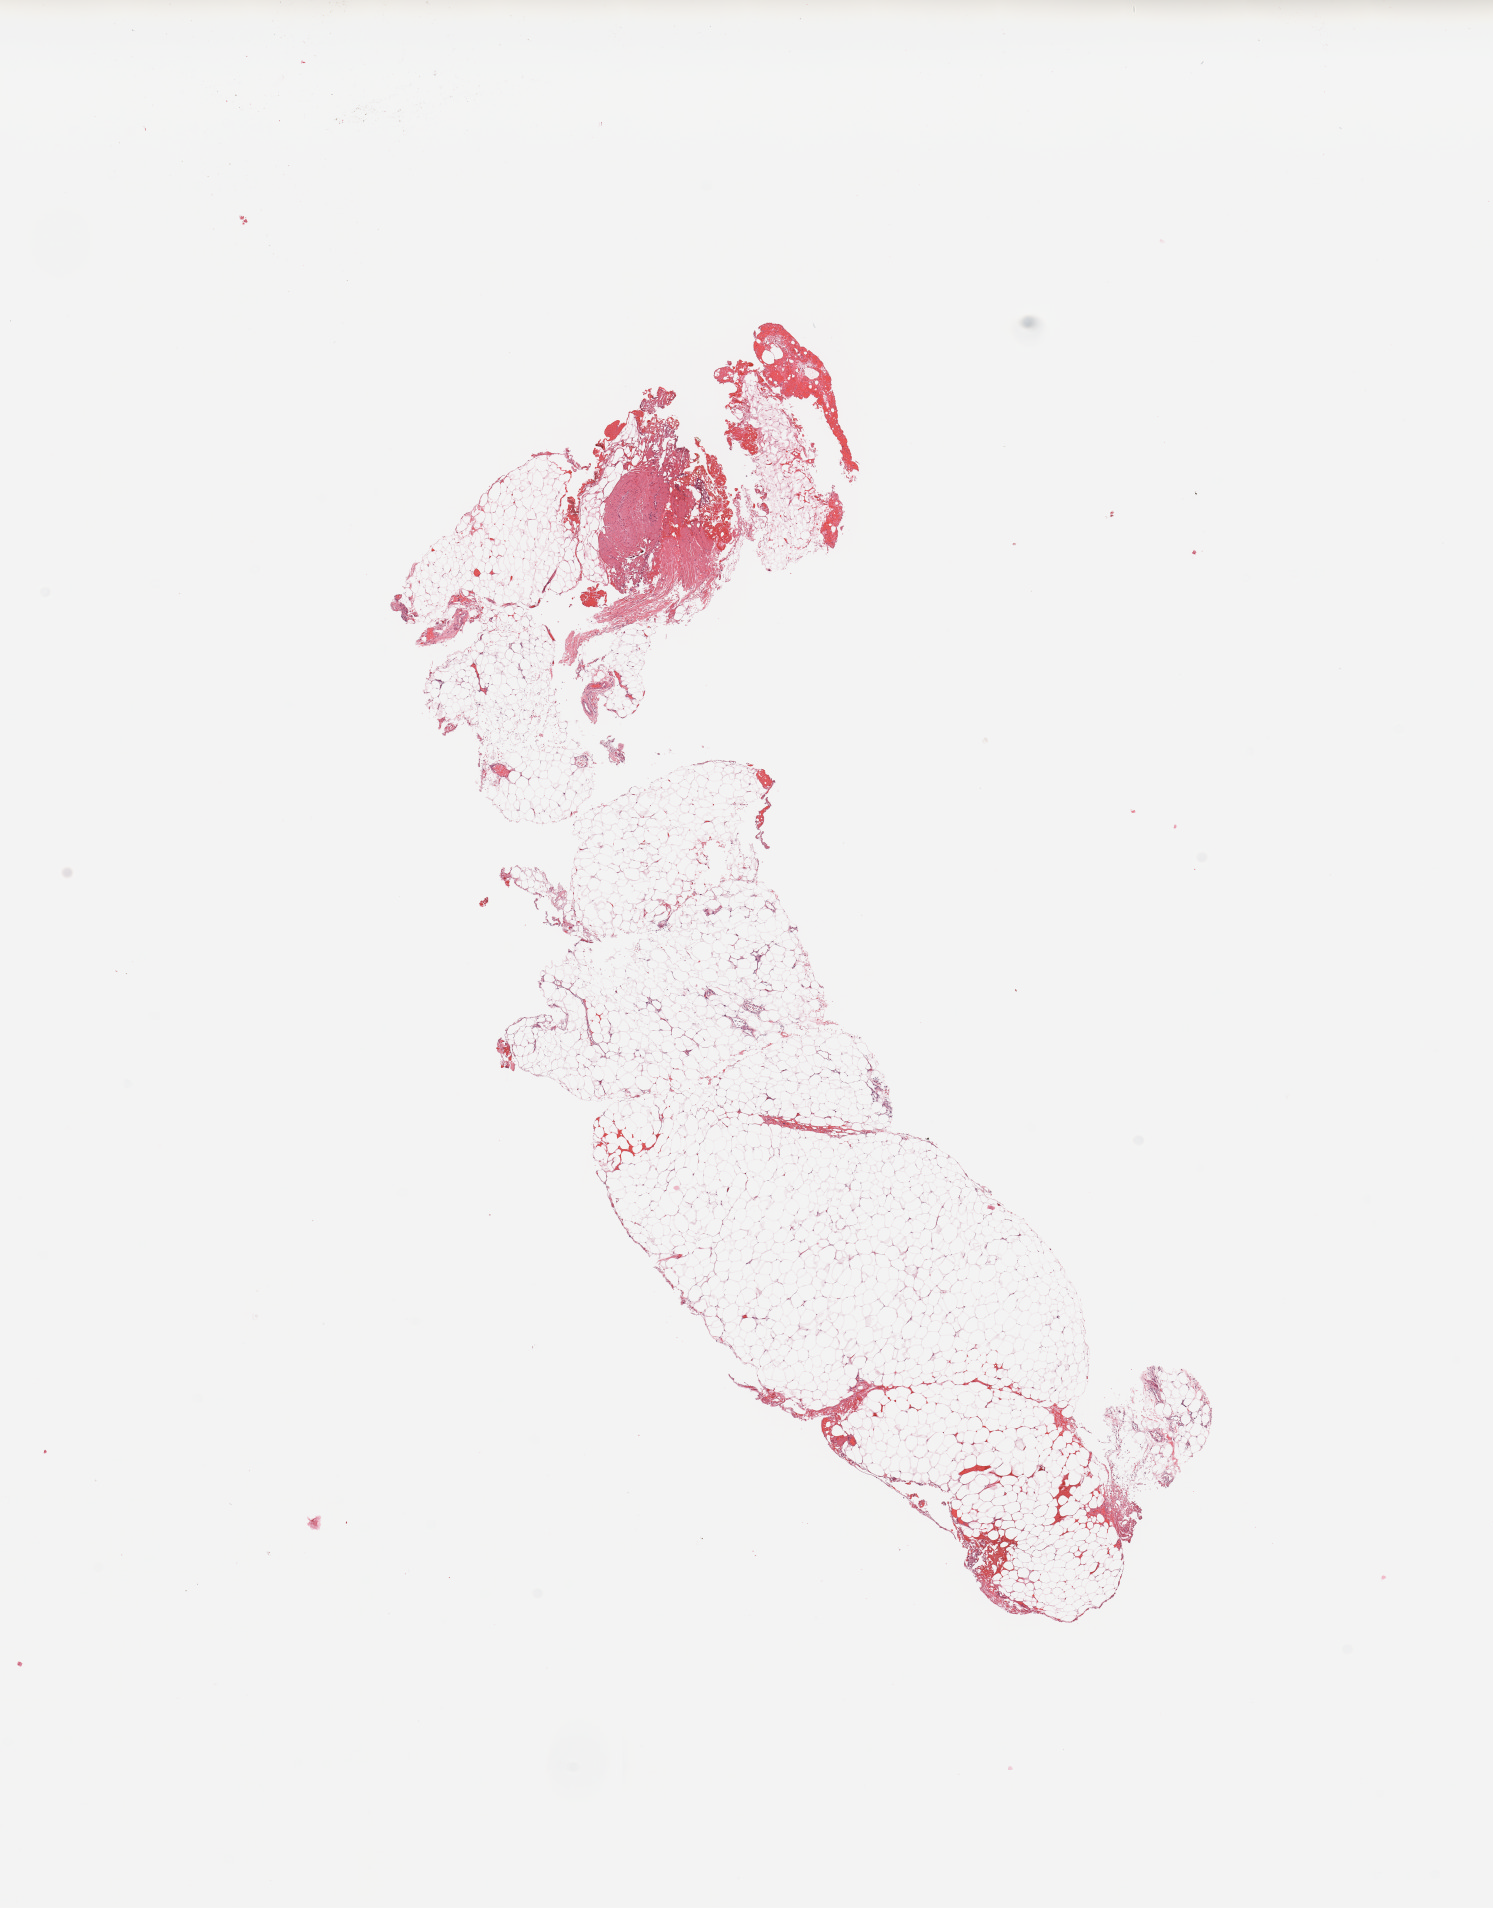
Digitized Hematoxylin and eosin (H&E) stained tissue section (whole slide) — low-resolution overview of the scanned area, about 11.8 x 15.1 mm (from a 20x scan), normal (non-tumour) tissue sample, kidney. 41-year-old male patient.
• this section: normal (non-tumour) tissue from the same patient
• patient diagnosis: Renal cell carcinoma, NOS